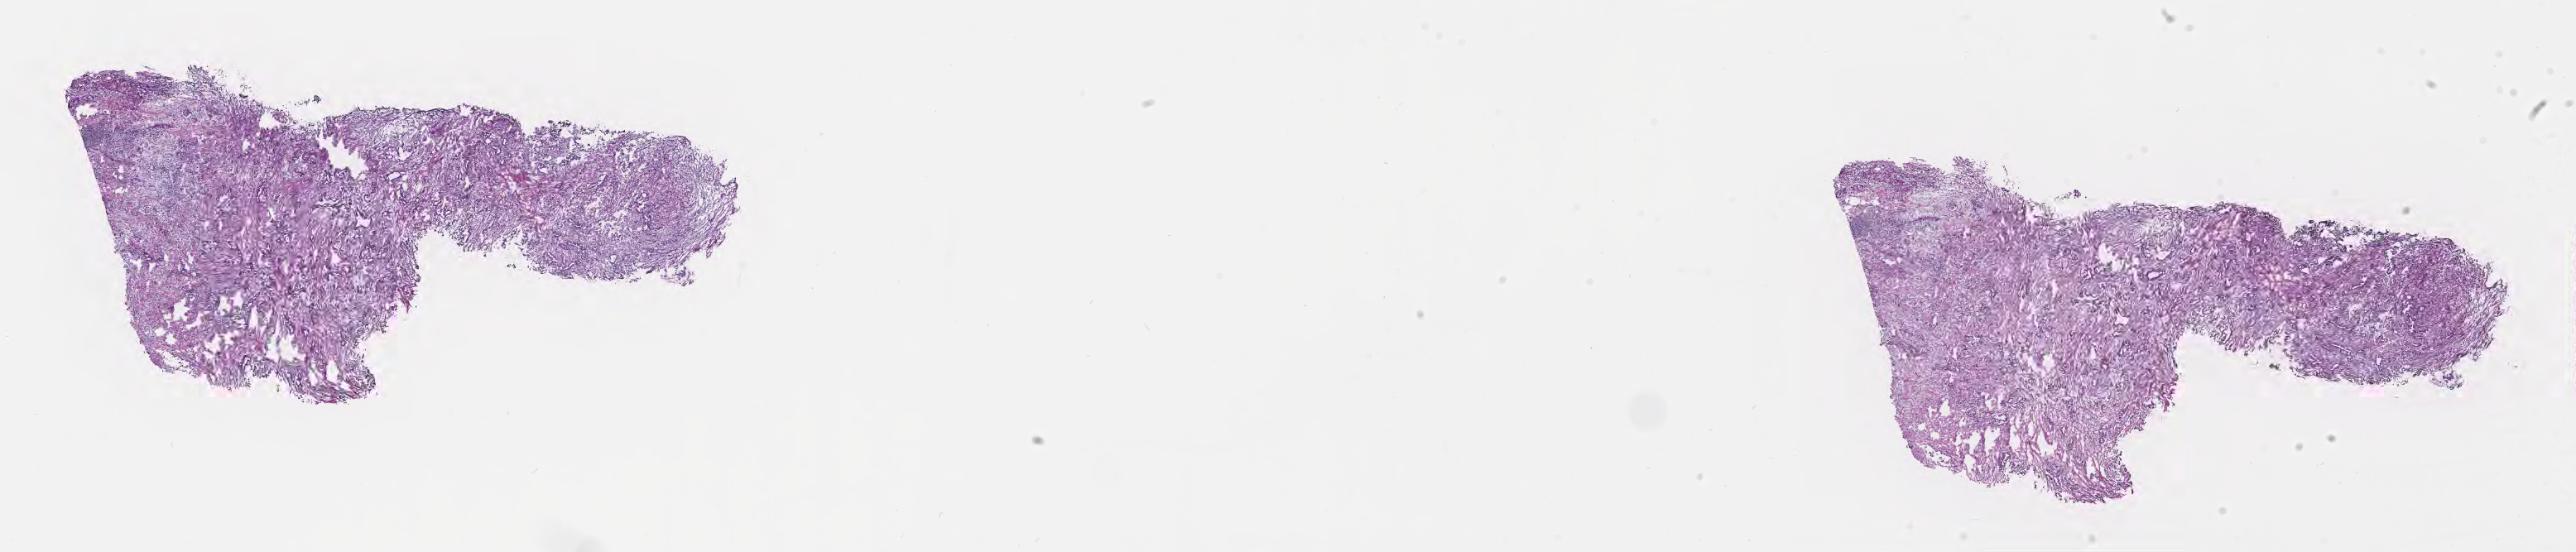
Digitized hematoxylin and eosin (H&E)-stained section, shown as a low-resolution overview of the whole scanned area (about 25.2 x 5.4 mm); cryosection; specimen: primary tumor; anatomic site: head of pancreas. Female patient; age at initial diagnosis 75 years.
Histologic diagnosis: Infiltrating duct carcinoma, NOS.